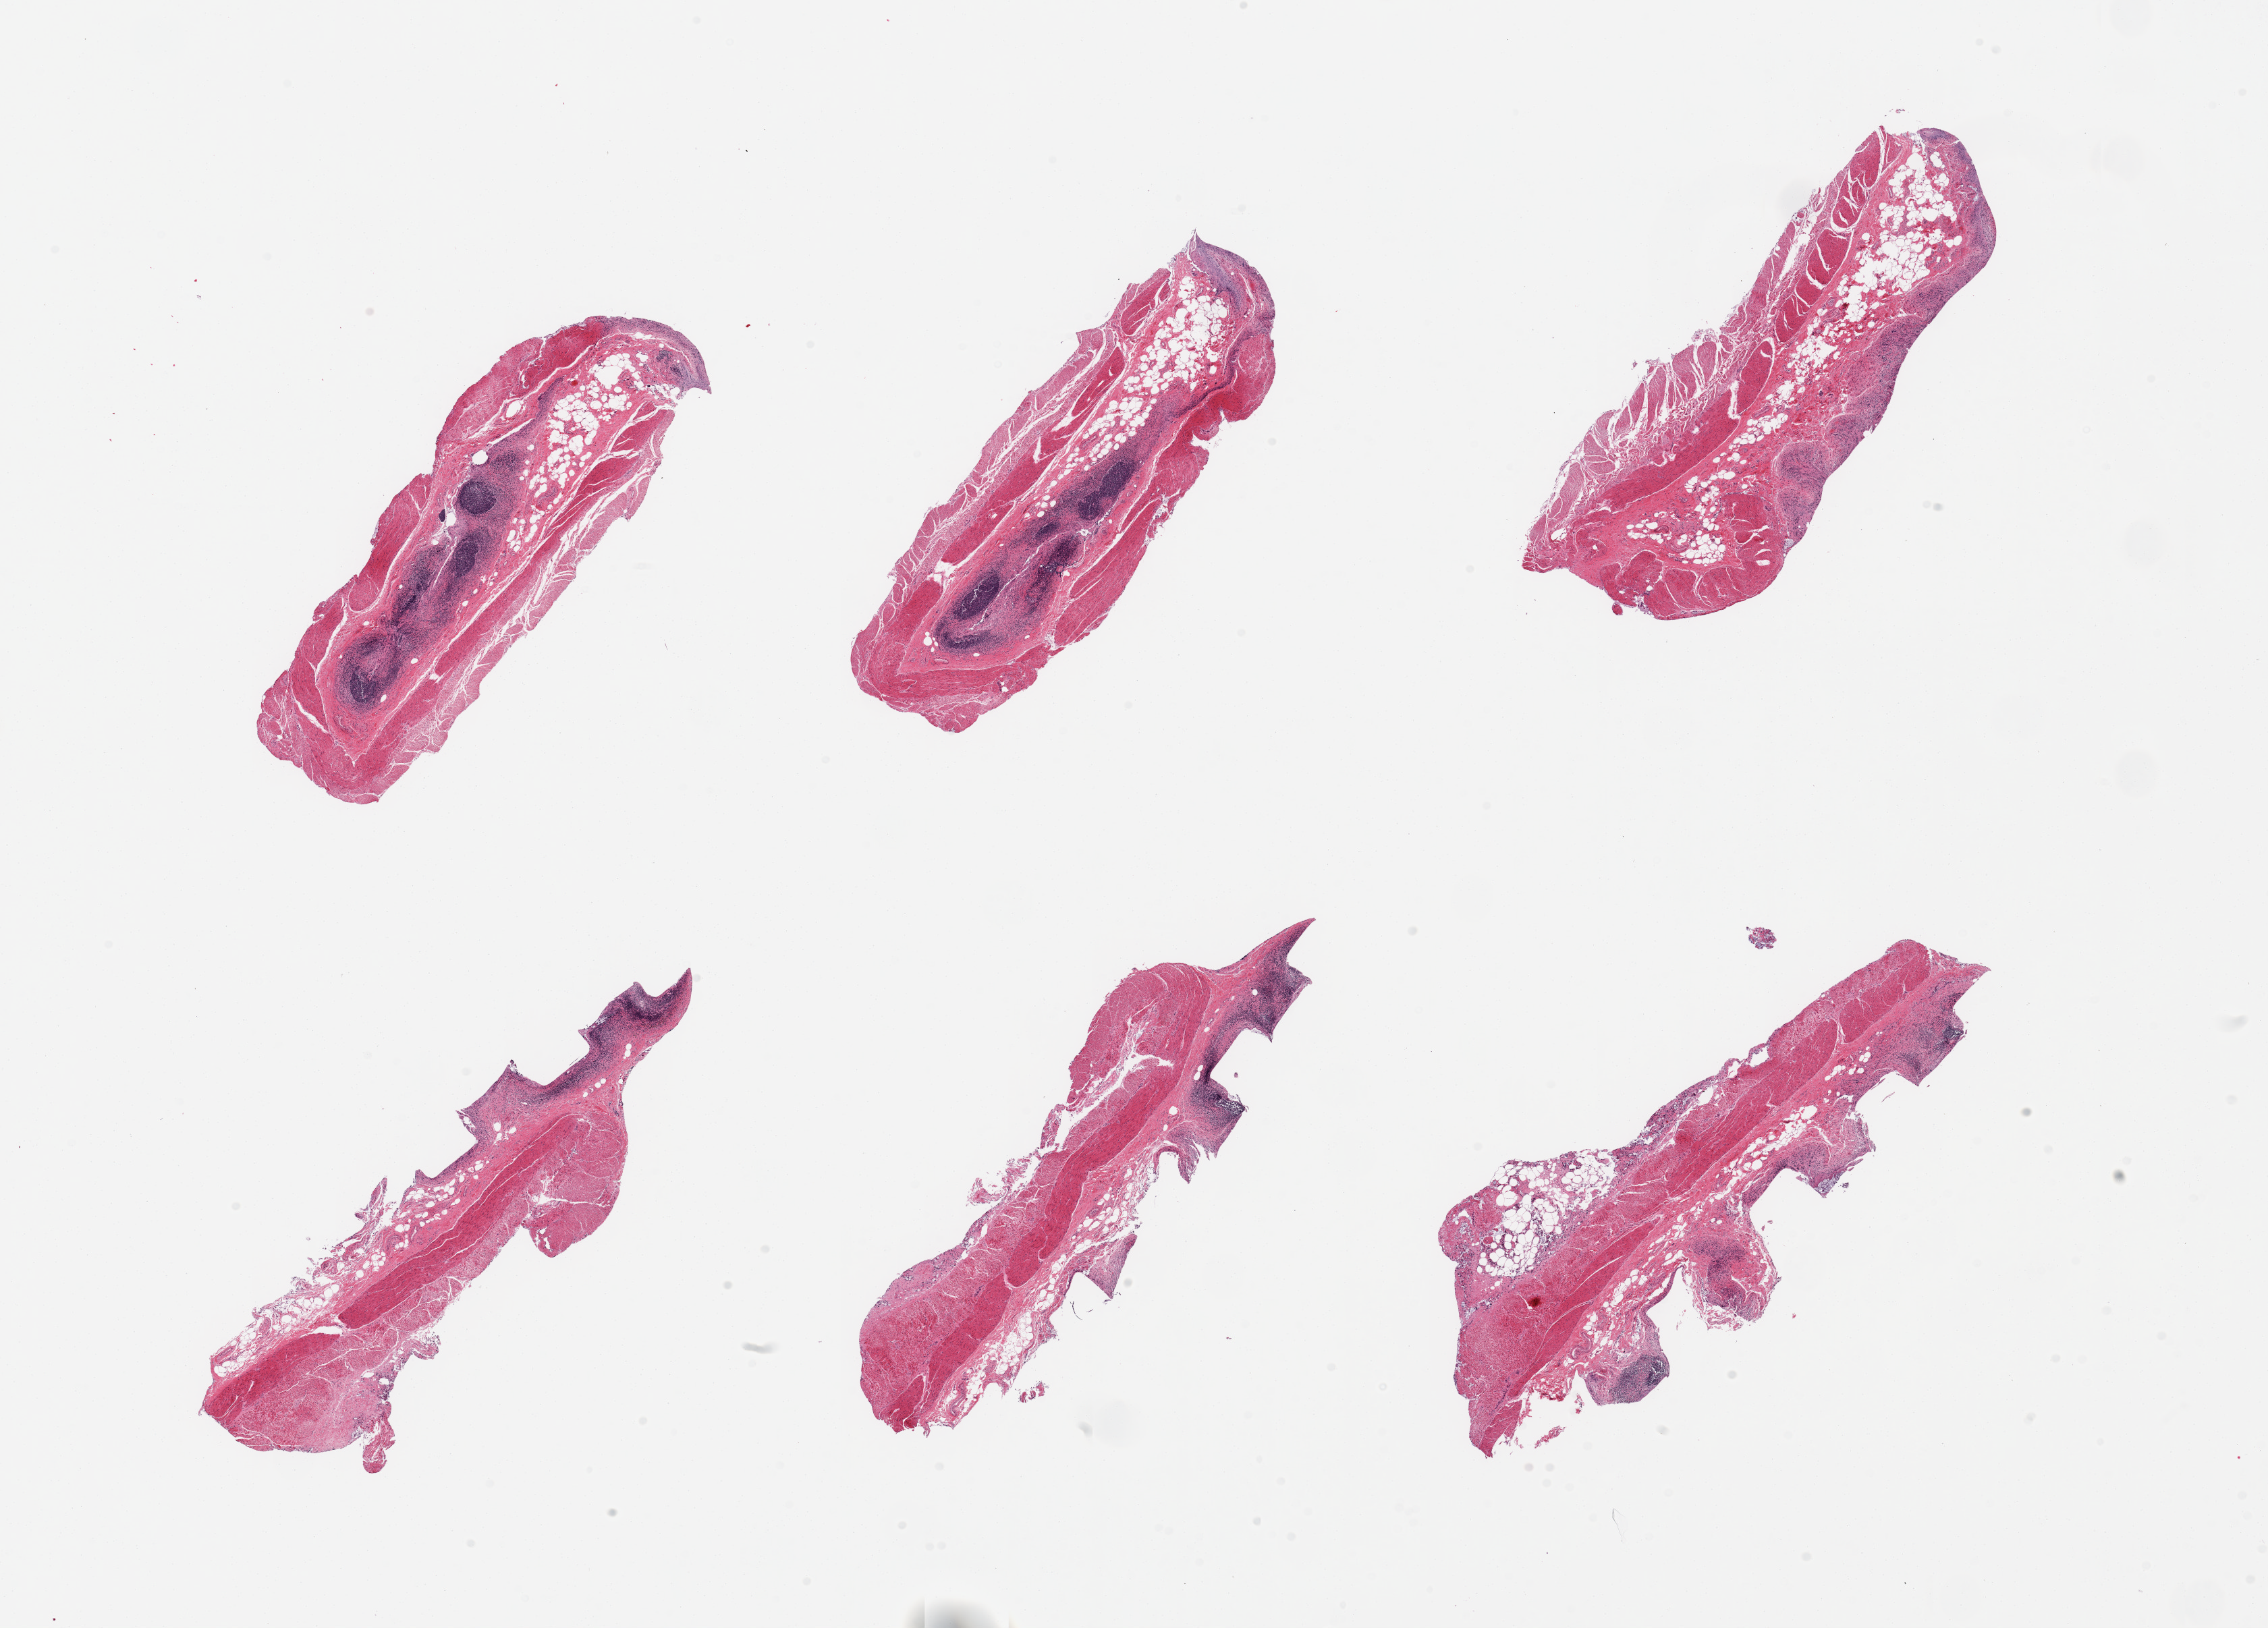
Digitized H&E-stained section — low-resolution overview of the scanned area, about 26.6 x 19.1 mm. Male donor.
Specimen: PAXgene-fixed, paraffin-embedded tissue; sampled site (target tissue): ileum; donor tissue sample.